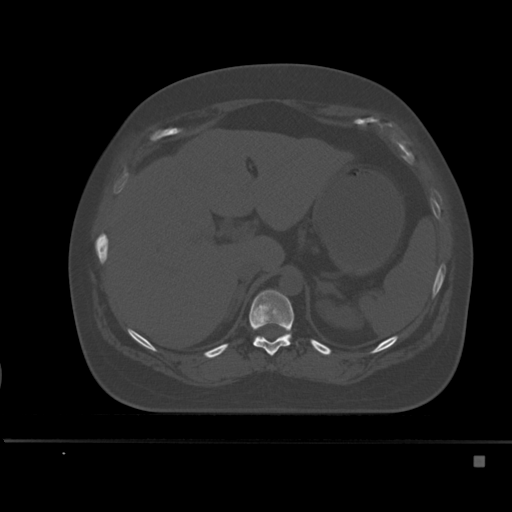
CT including the spine, one axial slice; bone window (W 1800 / L 400 HU); 512 × 512 image matrix. Female patient, age 33 years. From the clinical record (not read from this slice): primary cancer: breast; vertebrae with lytic lesions (as recorded): T1.
Structures marked on this image (semi-automatically segmented with operator editing):
- T11 vertebra: bounding box (x1, y1, x2, y2) in pixels: (249, 290, 294, 356)